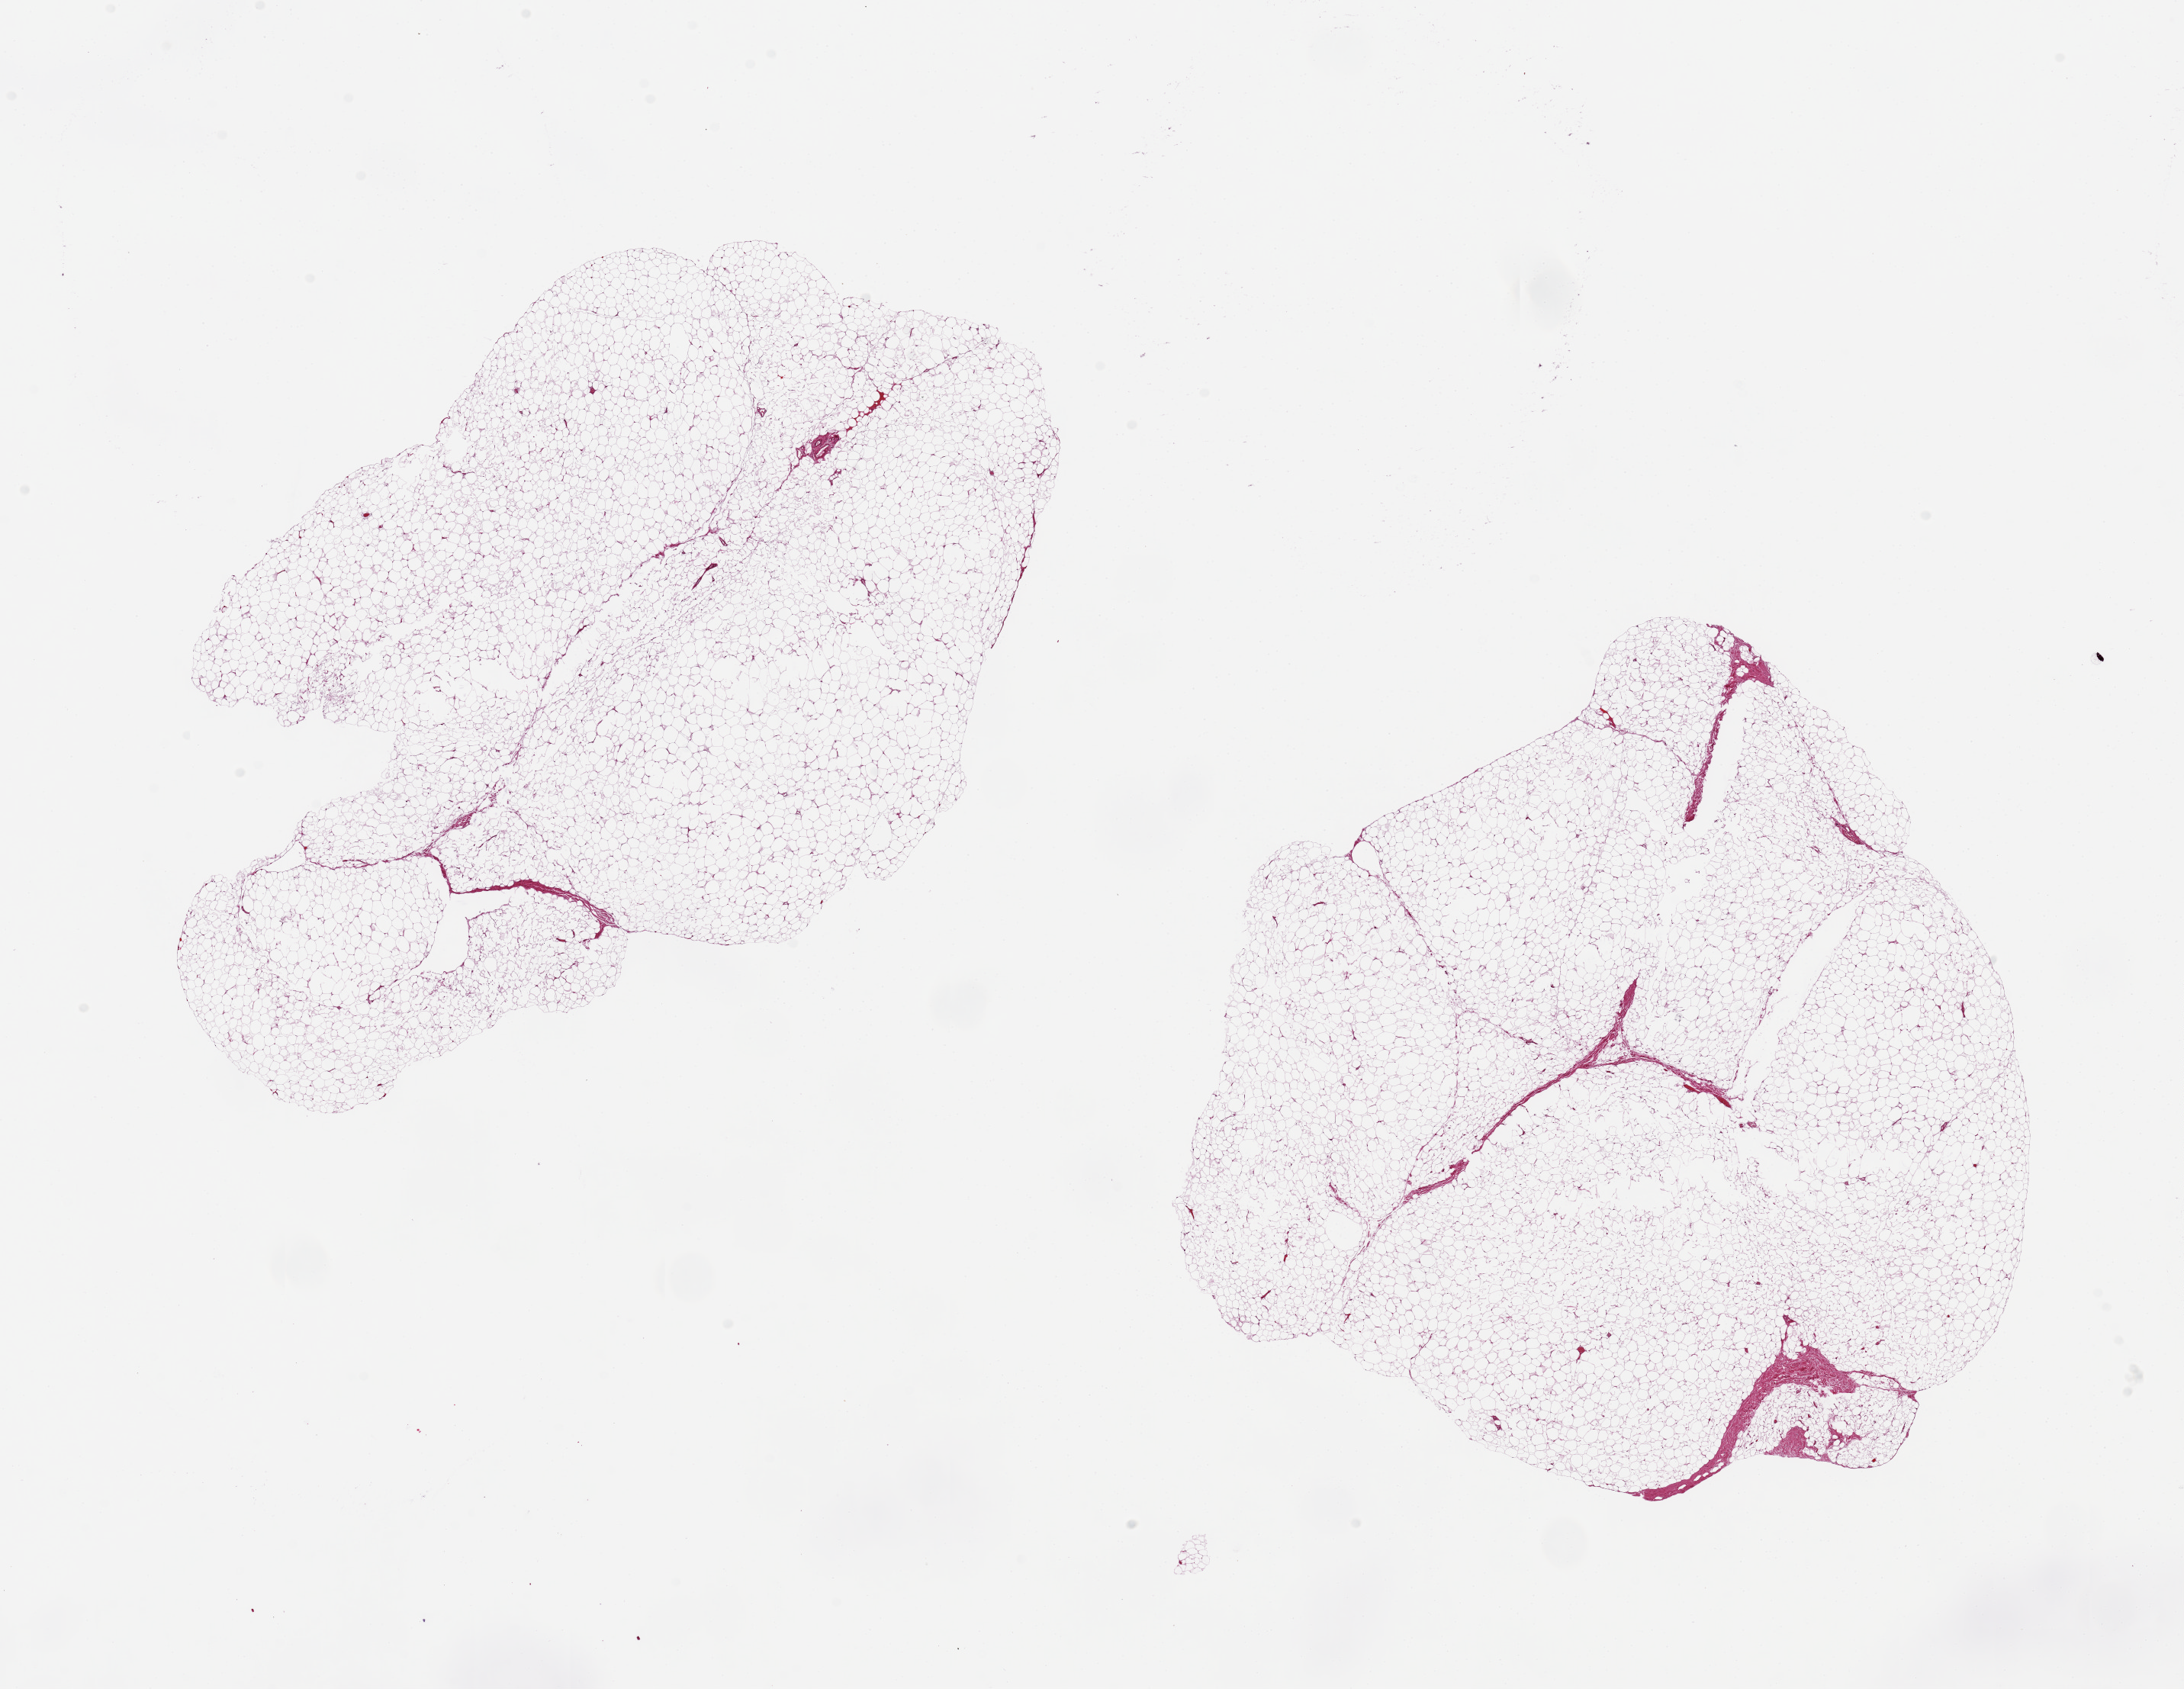
Digitized haematoxylin and eosin-stained section — whole scanned area (about 22.6 x 17.5 mm, slide scanned at 20x) shown as a low-resolution overview; PAXgene-fixed paraffin-embedded (PFPE) section; target tissue: breast; tissue donor sample. Male donor.
Pathologist's review note for this sample: 2 pieces ~8x8mm, all fat, no ductal elements noted.